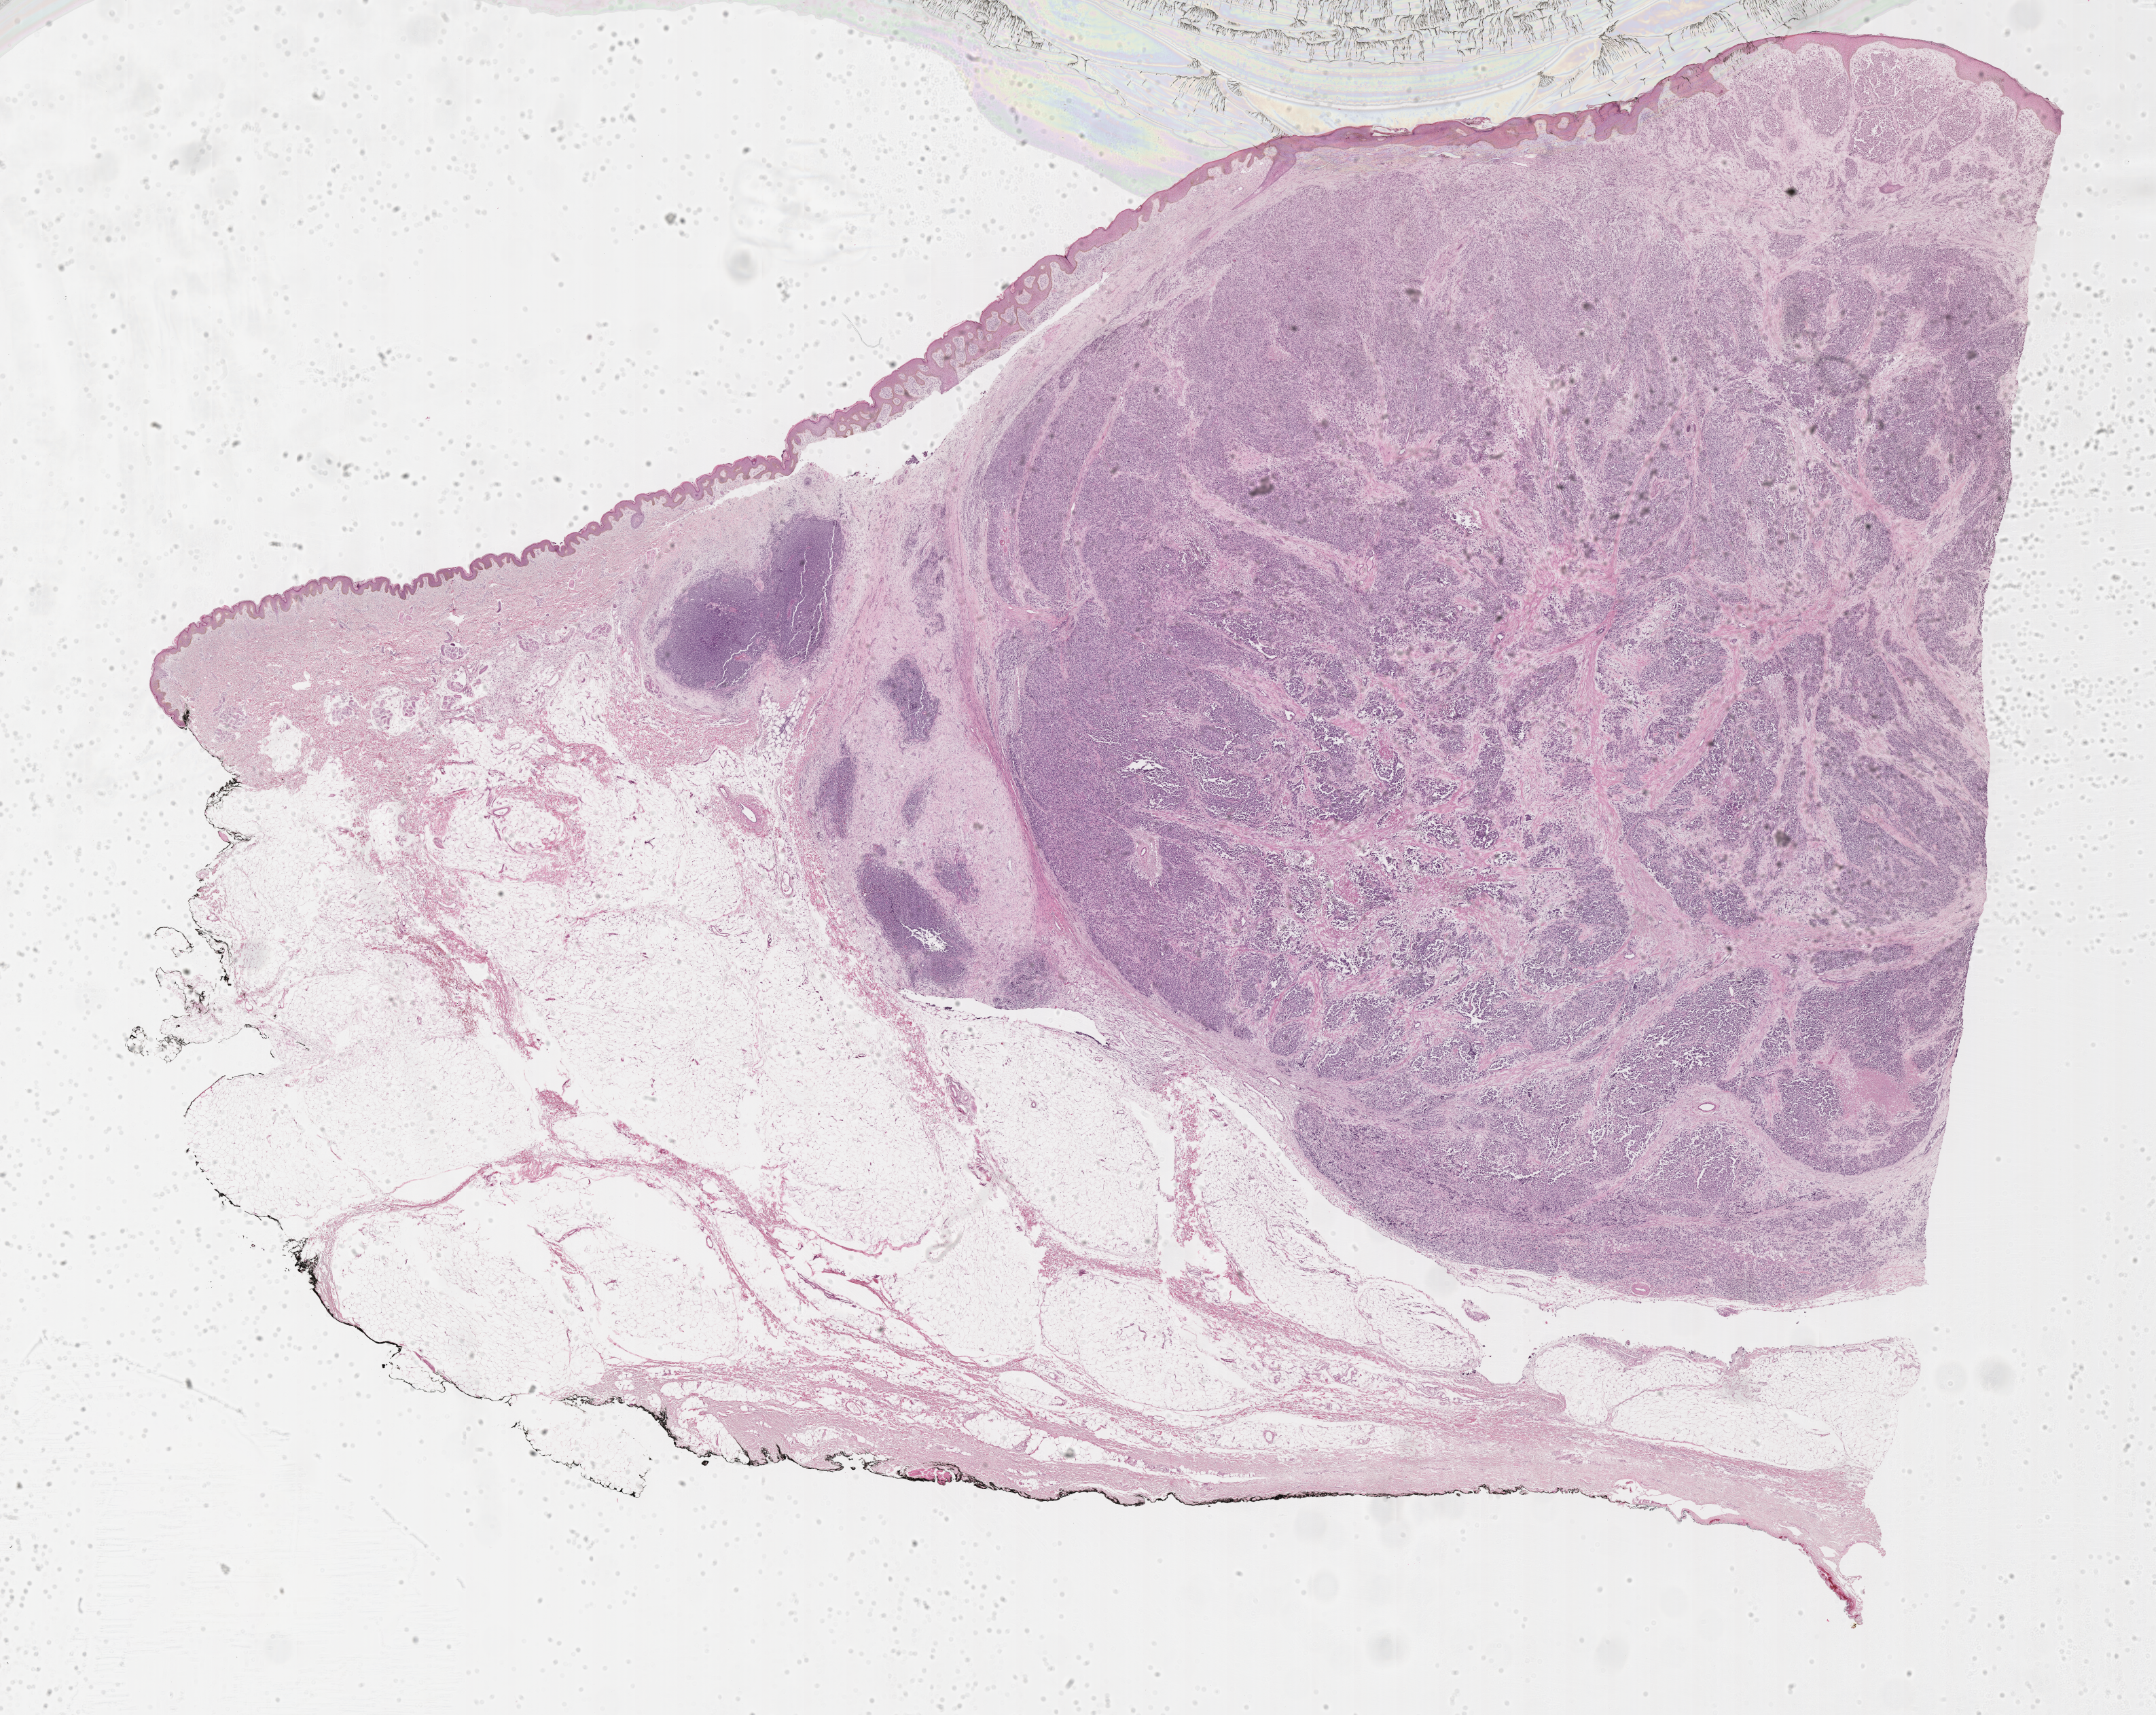
H&E whole-slide image of tumor tissue — shown as a low-resolution overview of the whole scanned area (about 25.7 x 20.4 mm). FFPE section. Site: chest-anterior. Male patient, age at diagnosis 1.6 years.
Primary site (case record): chest Wall. Stage (as recorded): 3. Metastatic status at presentation (as recorded): non-metastatic (confirmed). Diagnosis: rhabdomyosarcoma; histological classification: alveolar rhabdomyosarcoma.